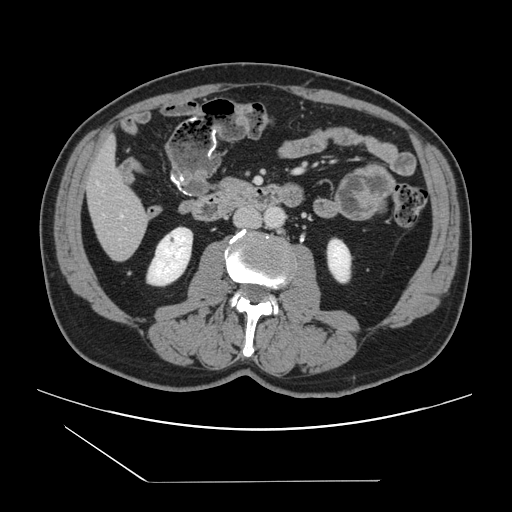
Contrast-enhanced abdominal CT, one axial slice; slice 33 of 157 in the series (ordered by position); 120 kVp; intravenous contrast given; soft-tissue window (W 400 / L 40 HU); 2.5 mm slice thickness; 512 × 512 image matrix. Male patient, age 61 years. From the clinical record (not read from this slice): diagnosis: colorectal cancer liver metastases, imaged before liver resection; multiple liver metastases: yes; largest metastasis: 5.5 cm; disease in both lobes: yes.
Structures marked on this image (manually delineated by an expert):
- hepatic veins: box from (x=120, y=215) to (x=123, y=217) px
- liver: (x=86, y=142)–(x=149, y=260)
- planned liver remnant (the part of the liver to remain after resection): (x=86, y=142)–(x=144, y=219)